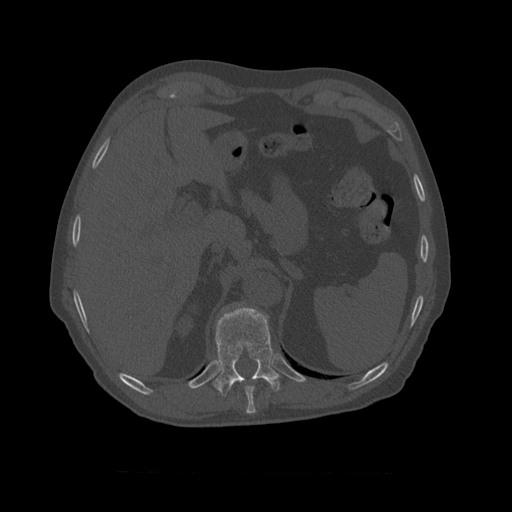
CT including the spine, one axial slice; bone window (W 1800 / L 400 HU); 1.25 mm slice thickness; 512 × 512 image matrix. Patient age 75 years. Case-level facts recorded for this patient, not image findings: primary cancer: prostate.
Outlined on this slice (semi-automatically segmented with operator editing):
- T10 vertebra: bounding box (x1, y1, x2, y2) in pixels: (213, 305, 281, 397)
- T9 vertebra: (245, 386, 256, 411)